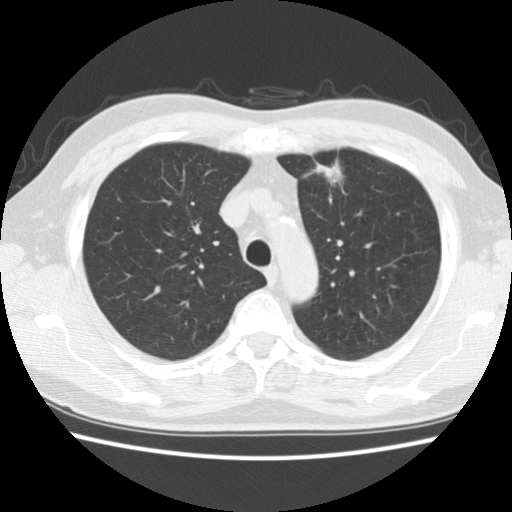
Axial slice from a low-dose chest CT screening exam. Second annual screen. Lung window (W 1500 / L -600 HU). Standard (soft-tissue) reconstruction kernel (STANDARD). Male participant, aged 63 years at enrolment. Former smoker at enrolment.
Expert-annotated lung lesion, box from (x=298, y=147) to (x=358, y=203) px. Reader record for this screening exam (exam-level; its link to the box is not recorded): non-calcified nodule or mass ≥4 mm, left upper lobe, 23 × 18 mm, spiculated (stellate) margins, soft tissue attenuation, pre-existing on the prior screen: yes; interval growth: yes. Official screen result: positive, other. Lung cancer was diagnosed 83 days after this screen: adenocarcinoma, NOS, left upper lobe, moderately differentiated (G2), stage IA (AJCC 6th edition), 14 mm at pathology.